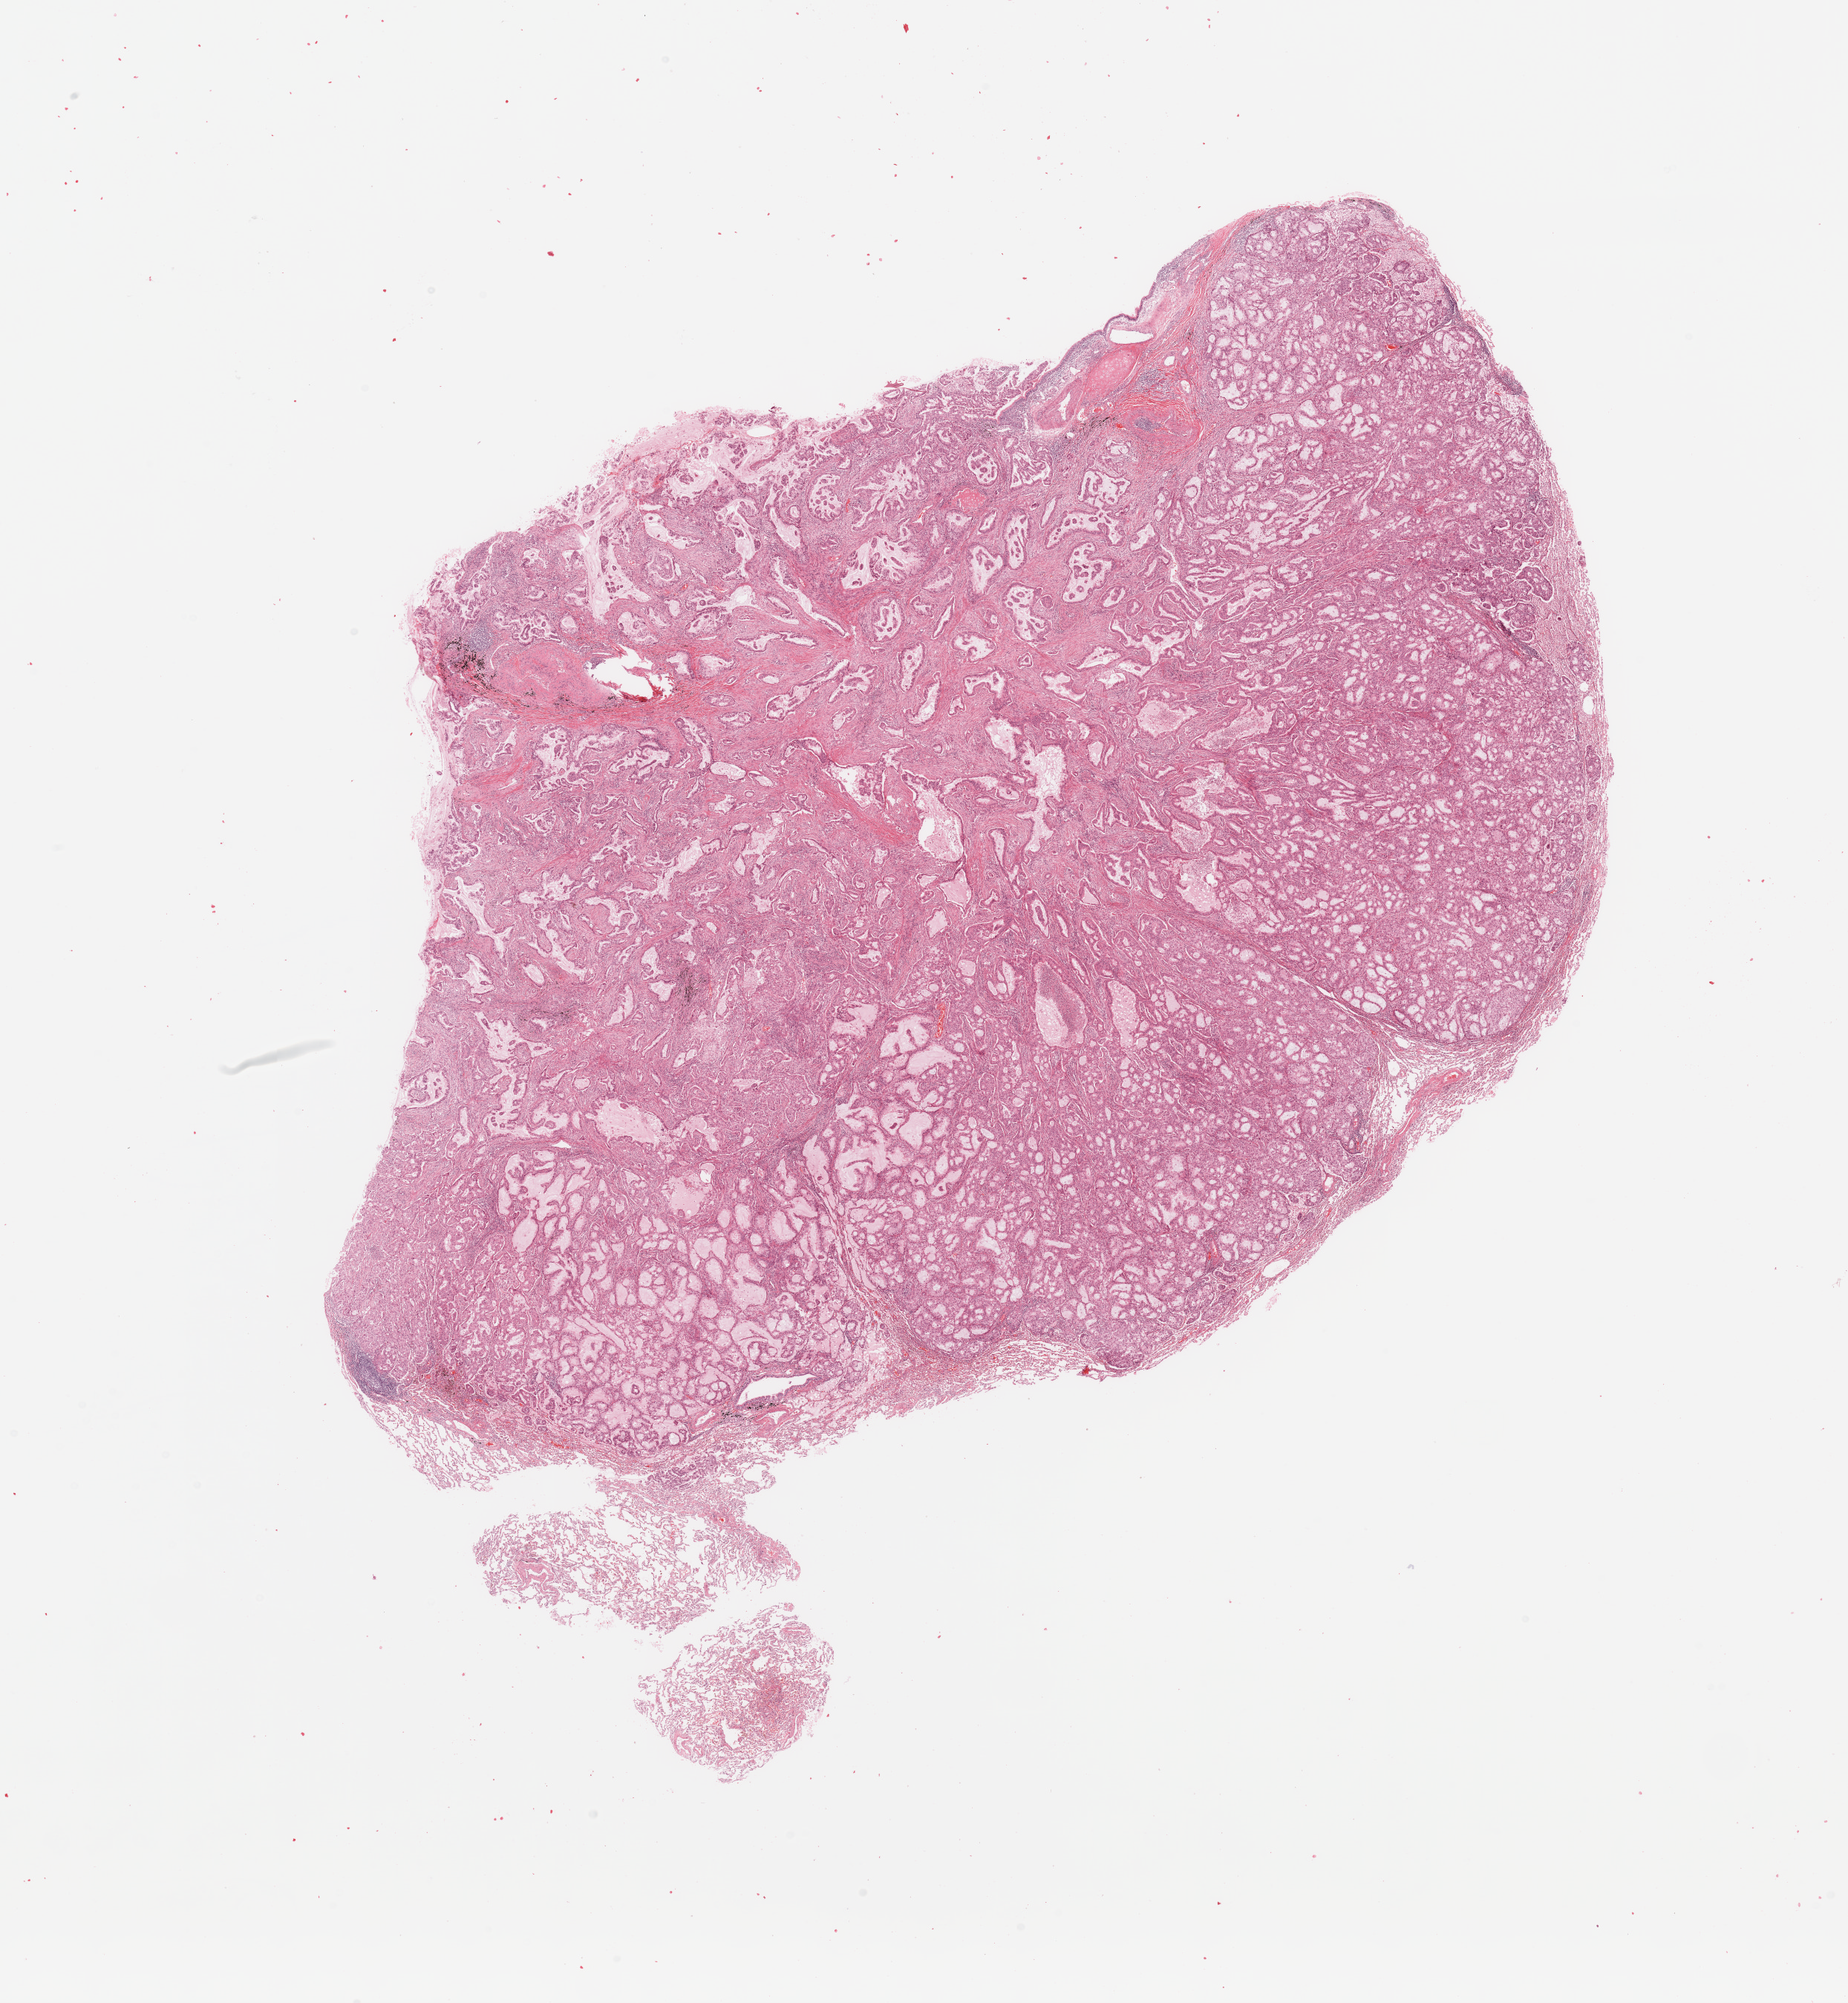
H&E-stained whole-slide image — whole scanned area (about 19.7 x 21.3 mm, acquisition: 20x scan) shown as a low-resolution overview; lung, tumour tissue. 48-year-old male patient. Histologic grade: G2 (moderately differentiated).
Histologic diagnosis: Adenocarcinoma, NOS. AJCC pathologic stage: IIIA.